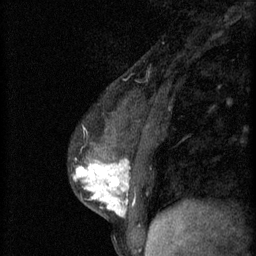
Breast MRI (dynamic contrast-enhanced), one sagittal slice. Slice 21 of 60 in the series (ordered by position). 3 images stored at this slice position (order not interpretable as contrast timing). 1.5 T. TE 4.2 ms, TR 11 ms. 2 mm slice thickness. 256 × 256 image matrix. Female patient, age 37 years.
Structures marked on this image (semi-automatically segmented with operator editing):
- analysis volume of interest (the breast-tissue region the enhancement analysis was run in; not a lesion): bounding box [x1, y1, x2, y2] px = [72, 138, 174, 221]
- tumour enhancement mask (voxels above the 70 % enhancement threshold inside the analysis volume of interest): [73, 160, 130, 217]